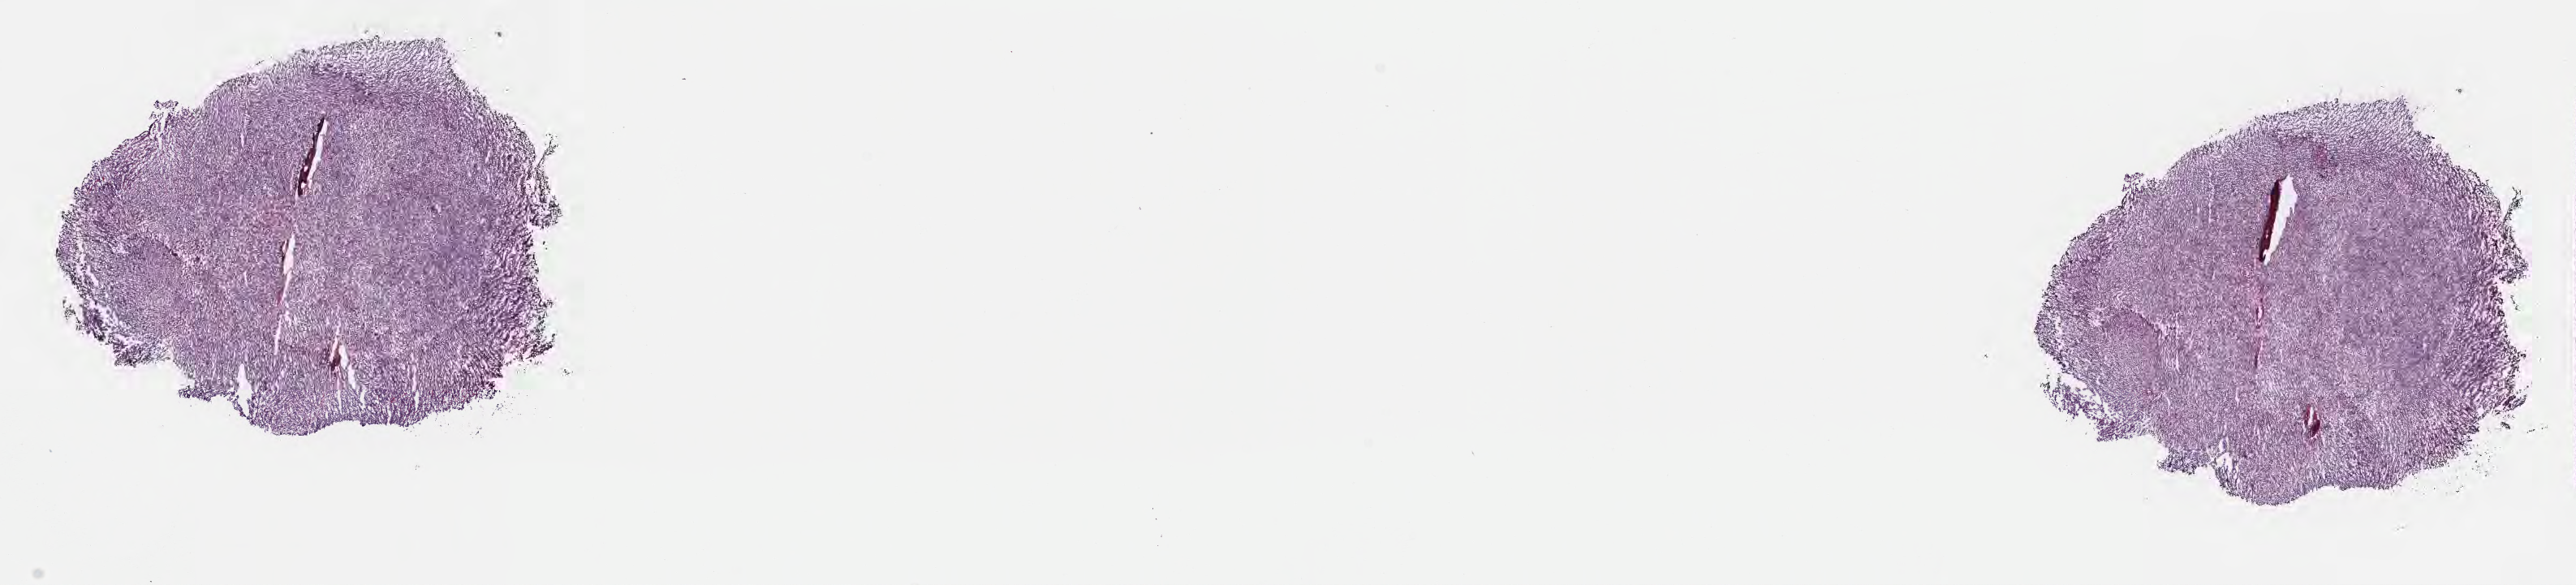
Digitized H&E-stained section — shown as a low-resolution overview of the whole scanned area (about 25.7 x 5.8 mm), frozen section (tissue freezing medium), primary tumor, anatomic site: mandible. Female patient; age at initial diagnosis 5 years. Pathologist review of this section (percent, as recorded): tumor cells 85%, tumor nuclei 85%, stromal cells 5%, necrosis 10%, normal cells 0%. Inflammatory infiltration, as recorded: lymphocyte infiltration 50%, monocyte infiltration 25%, neutrophil infiltration 5%.
Ann Arbor stage (patient): Stage III. Diagnosis: Burkitt lymphoma, NOS. Section: bottom of the tissue portion.